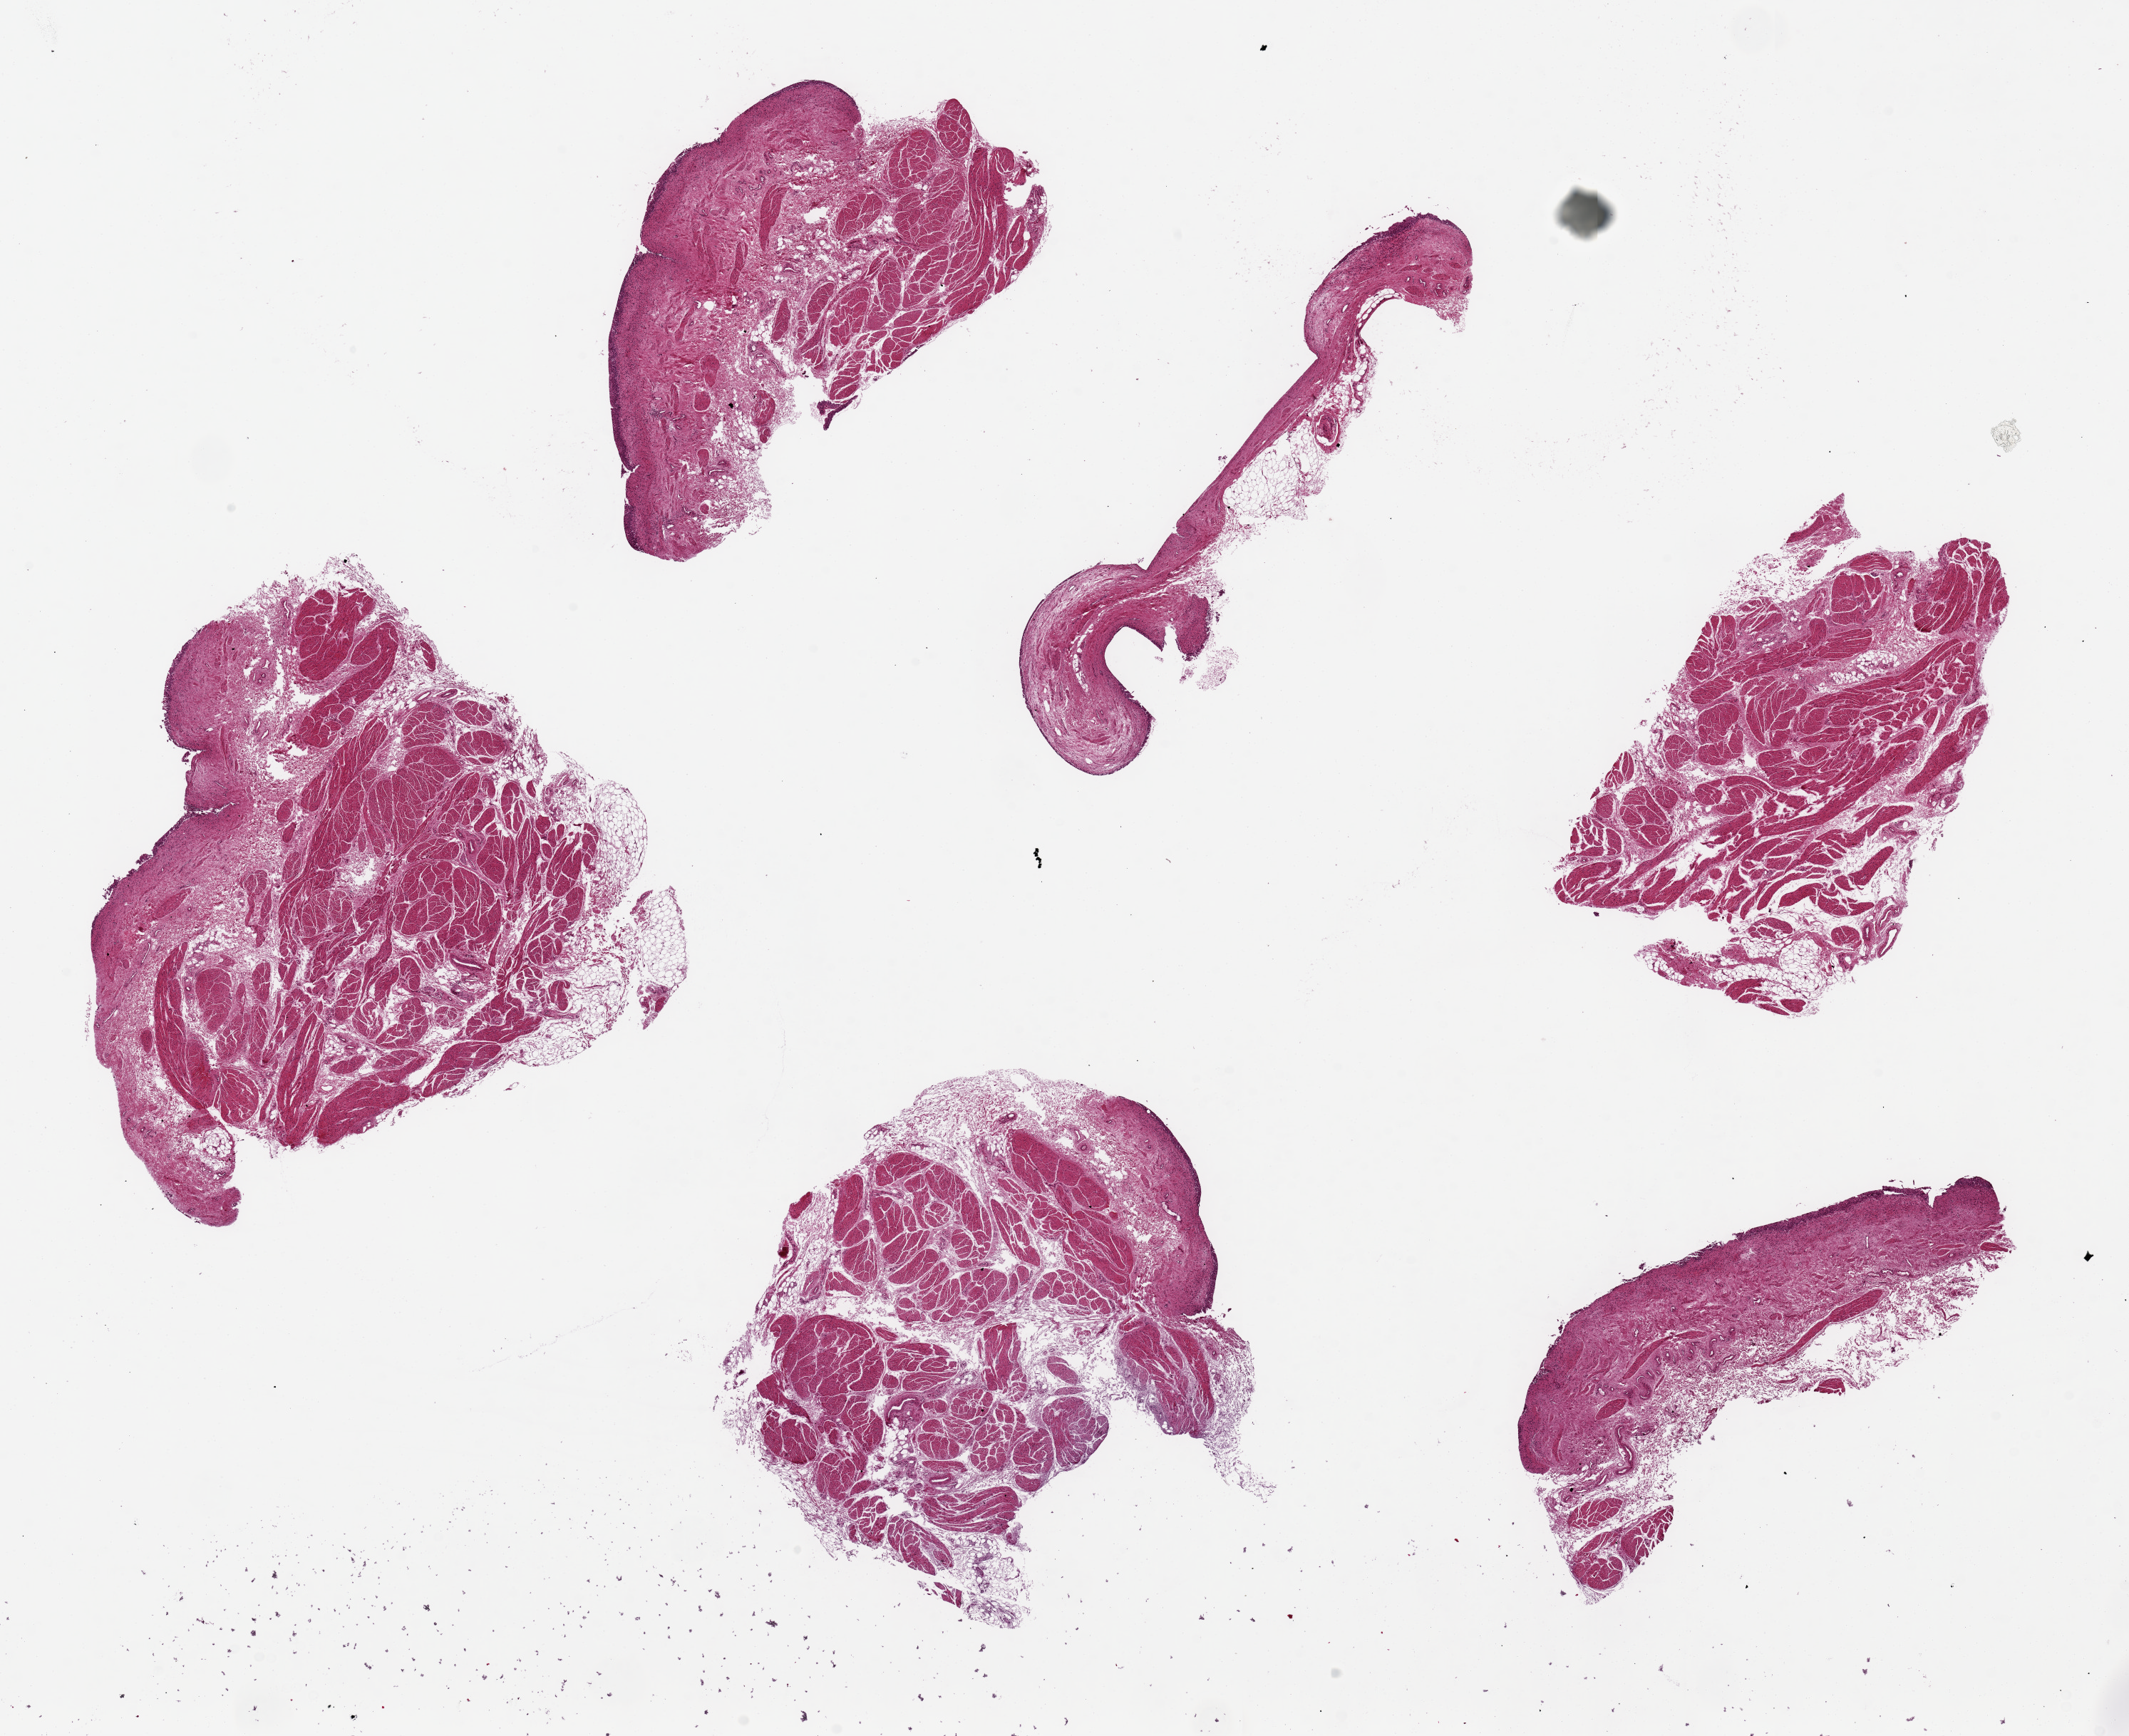
Digitized H&E-stained section, brightfield — a low-resolution overview of the entire scanned area, about 23.6 x 19.3 mm (acquisition: 20x scan). PAXgene-fixed, paraffin-embedded tissue. Sampled site (target tissue): urinary bladder. Donor tissue sample. Donor: female.
Pathologist's review note for this sample: 6 pieces, ~ 6x4mm, urothelium partly sloughed, <2% of thickness when present.